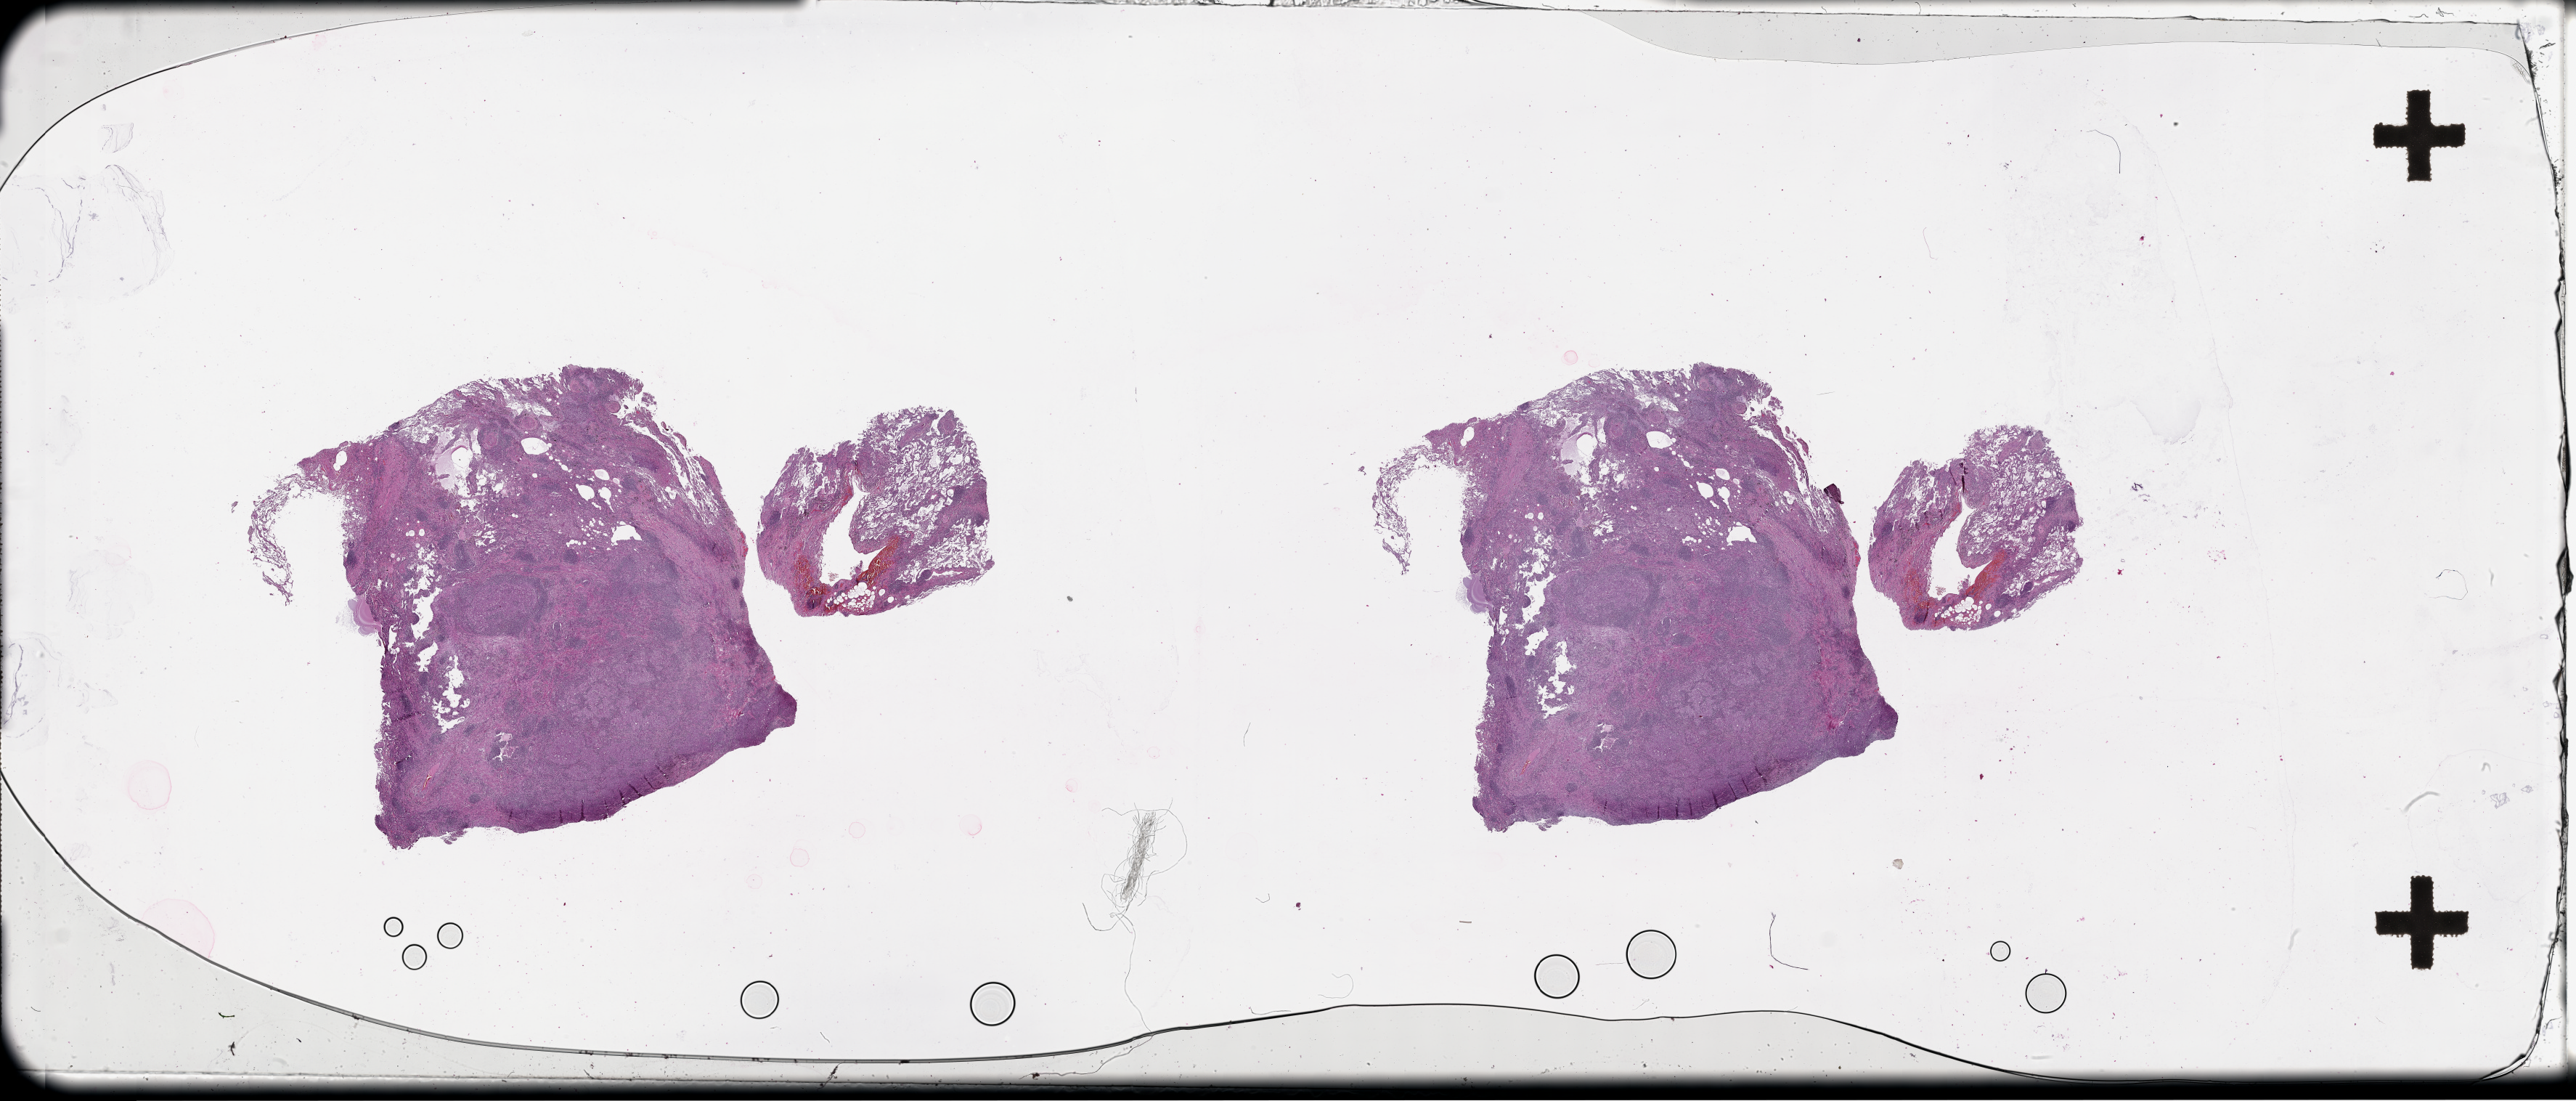
Digitized H&E tissue section (whole slide), a low-resolution overview of the entire scanned area, about 57.1 x 24.4 mm (acquisition: 20x scan), lung, tumour tissue. Patient: male, age 71 years.
Patient diagnosis (cohort enrolment): squamous cell carcinoma (lung).